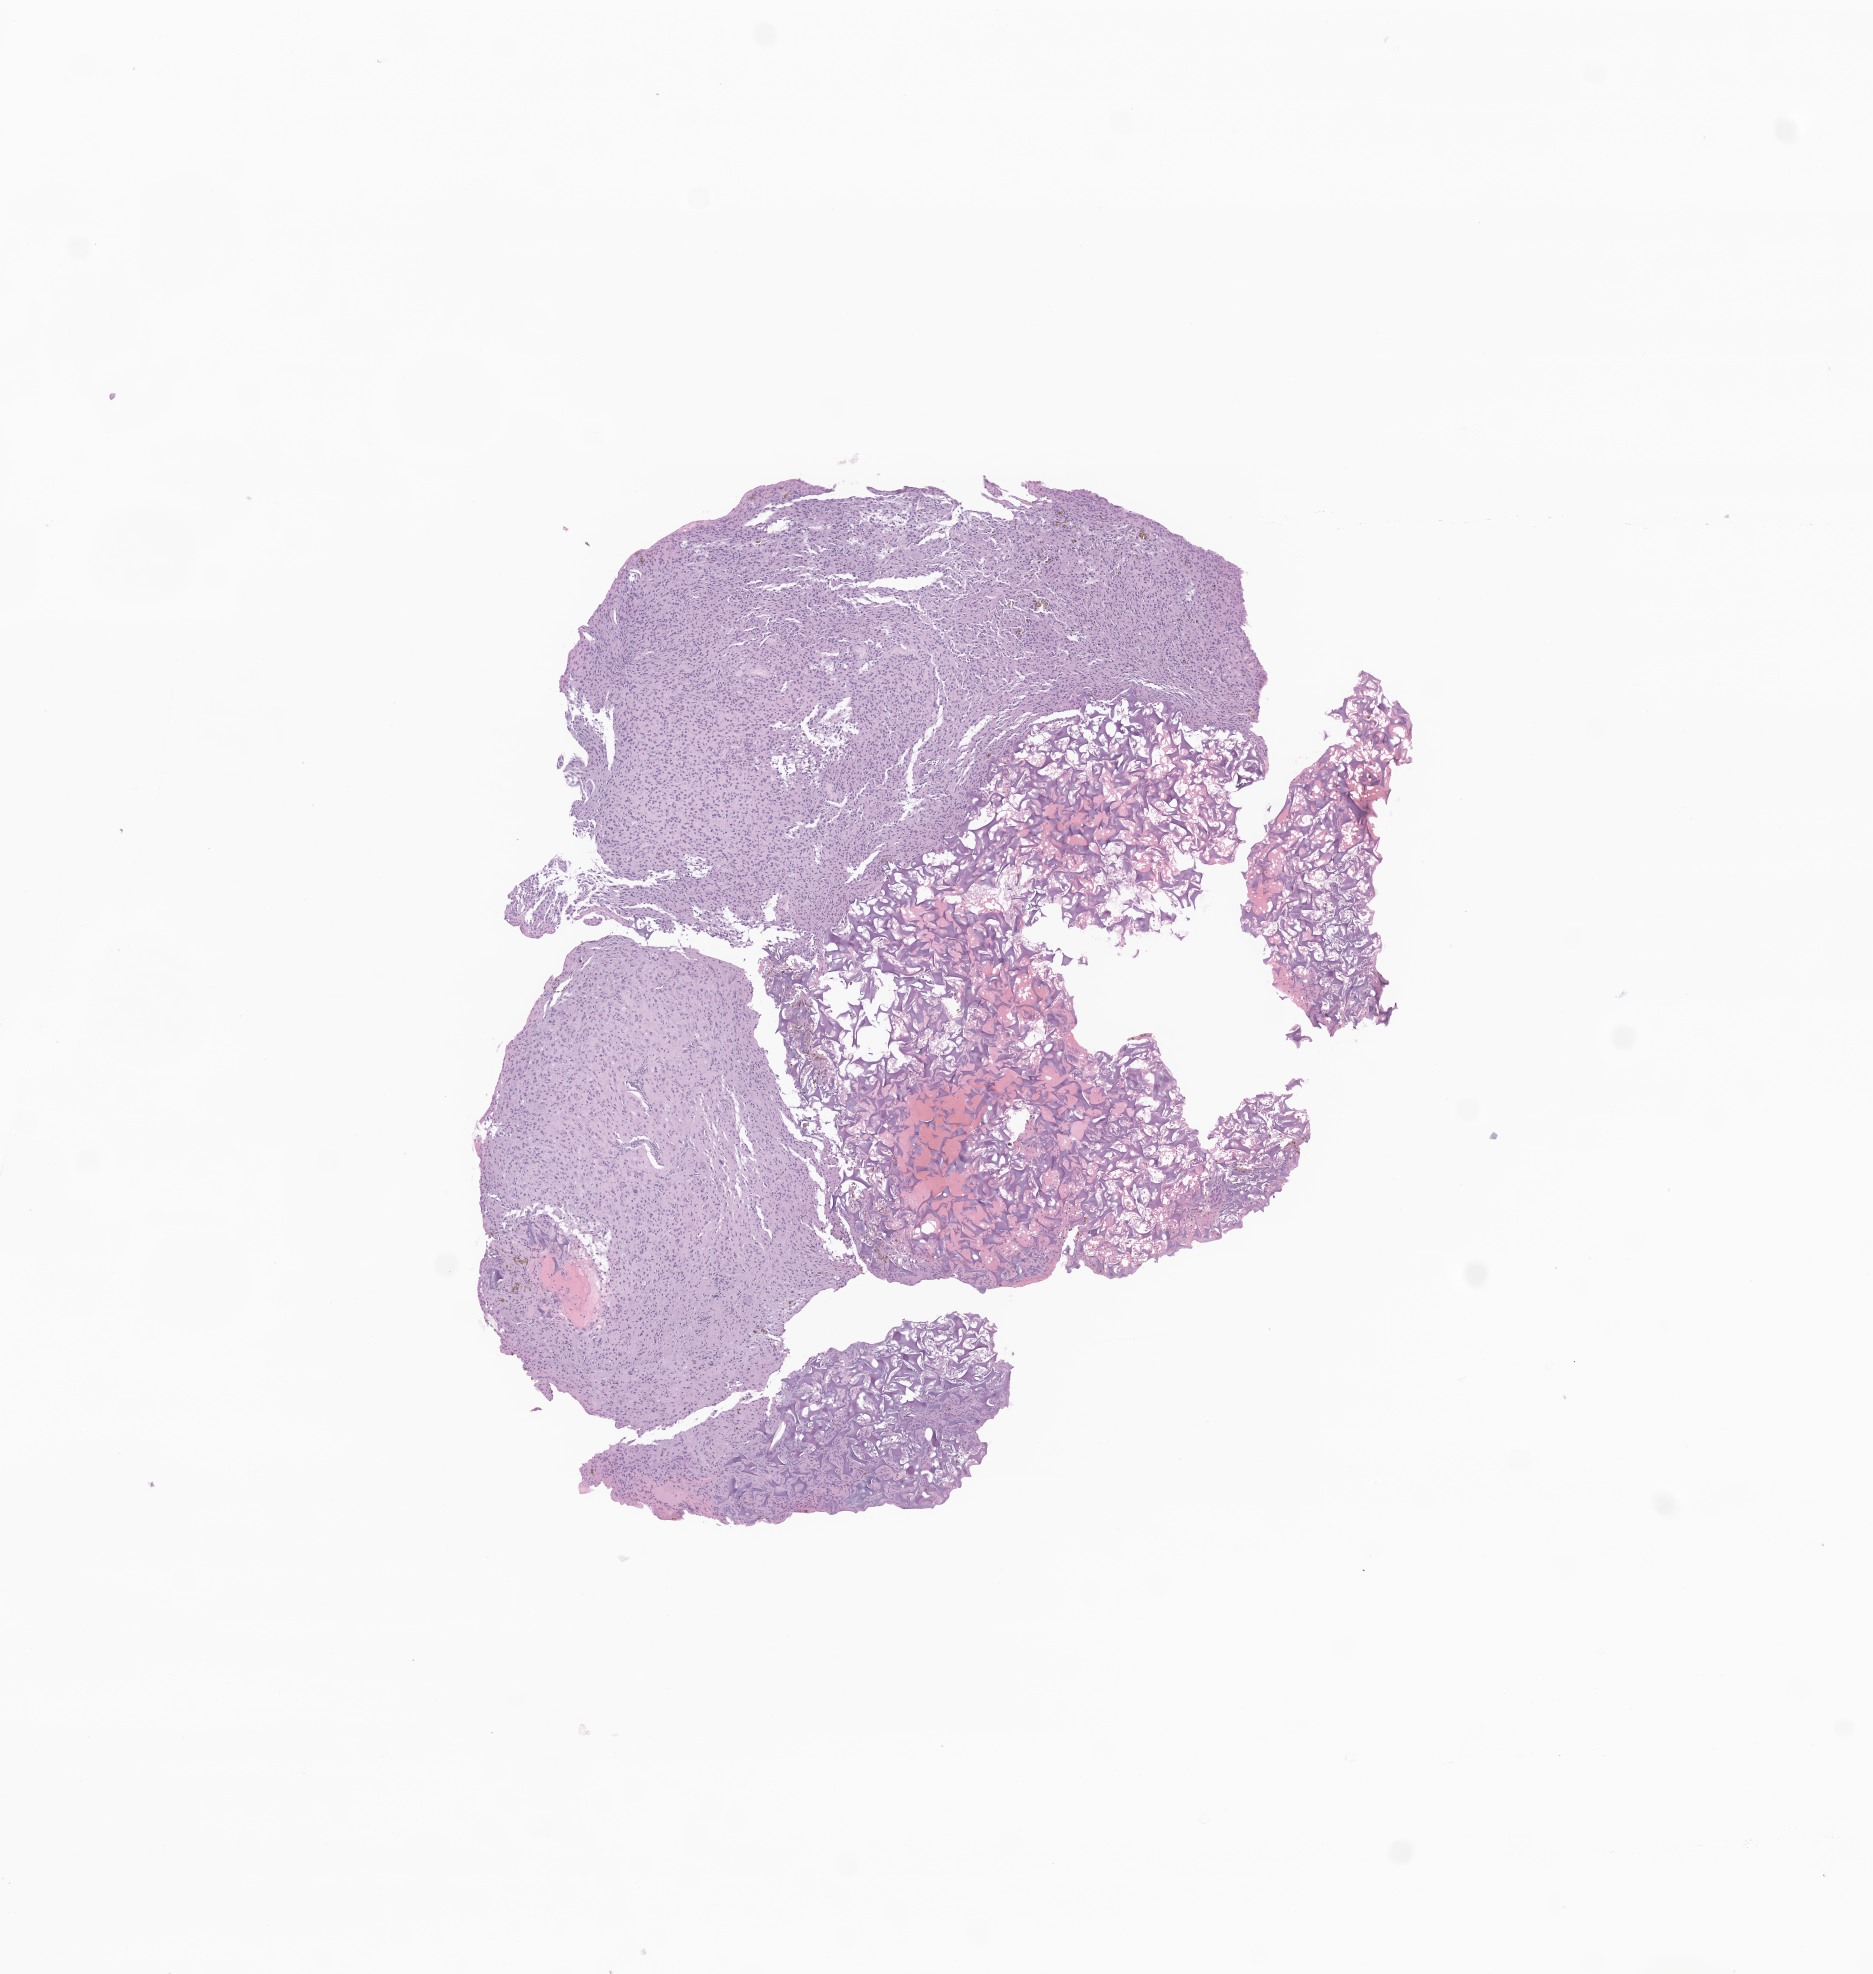
Whole-slide image, H&E stain of tumor tissue from the brain, shown as a low-resolution overview of the whole scanned area (about 7.9 x 8.3 mm). FFPE section. Patient male; age 36 months (3 years).
Recorded diagnosis: Glioma, malignant.